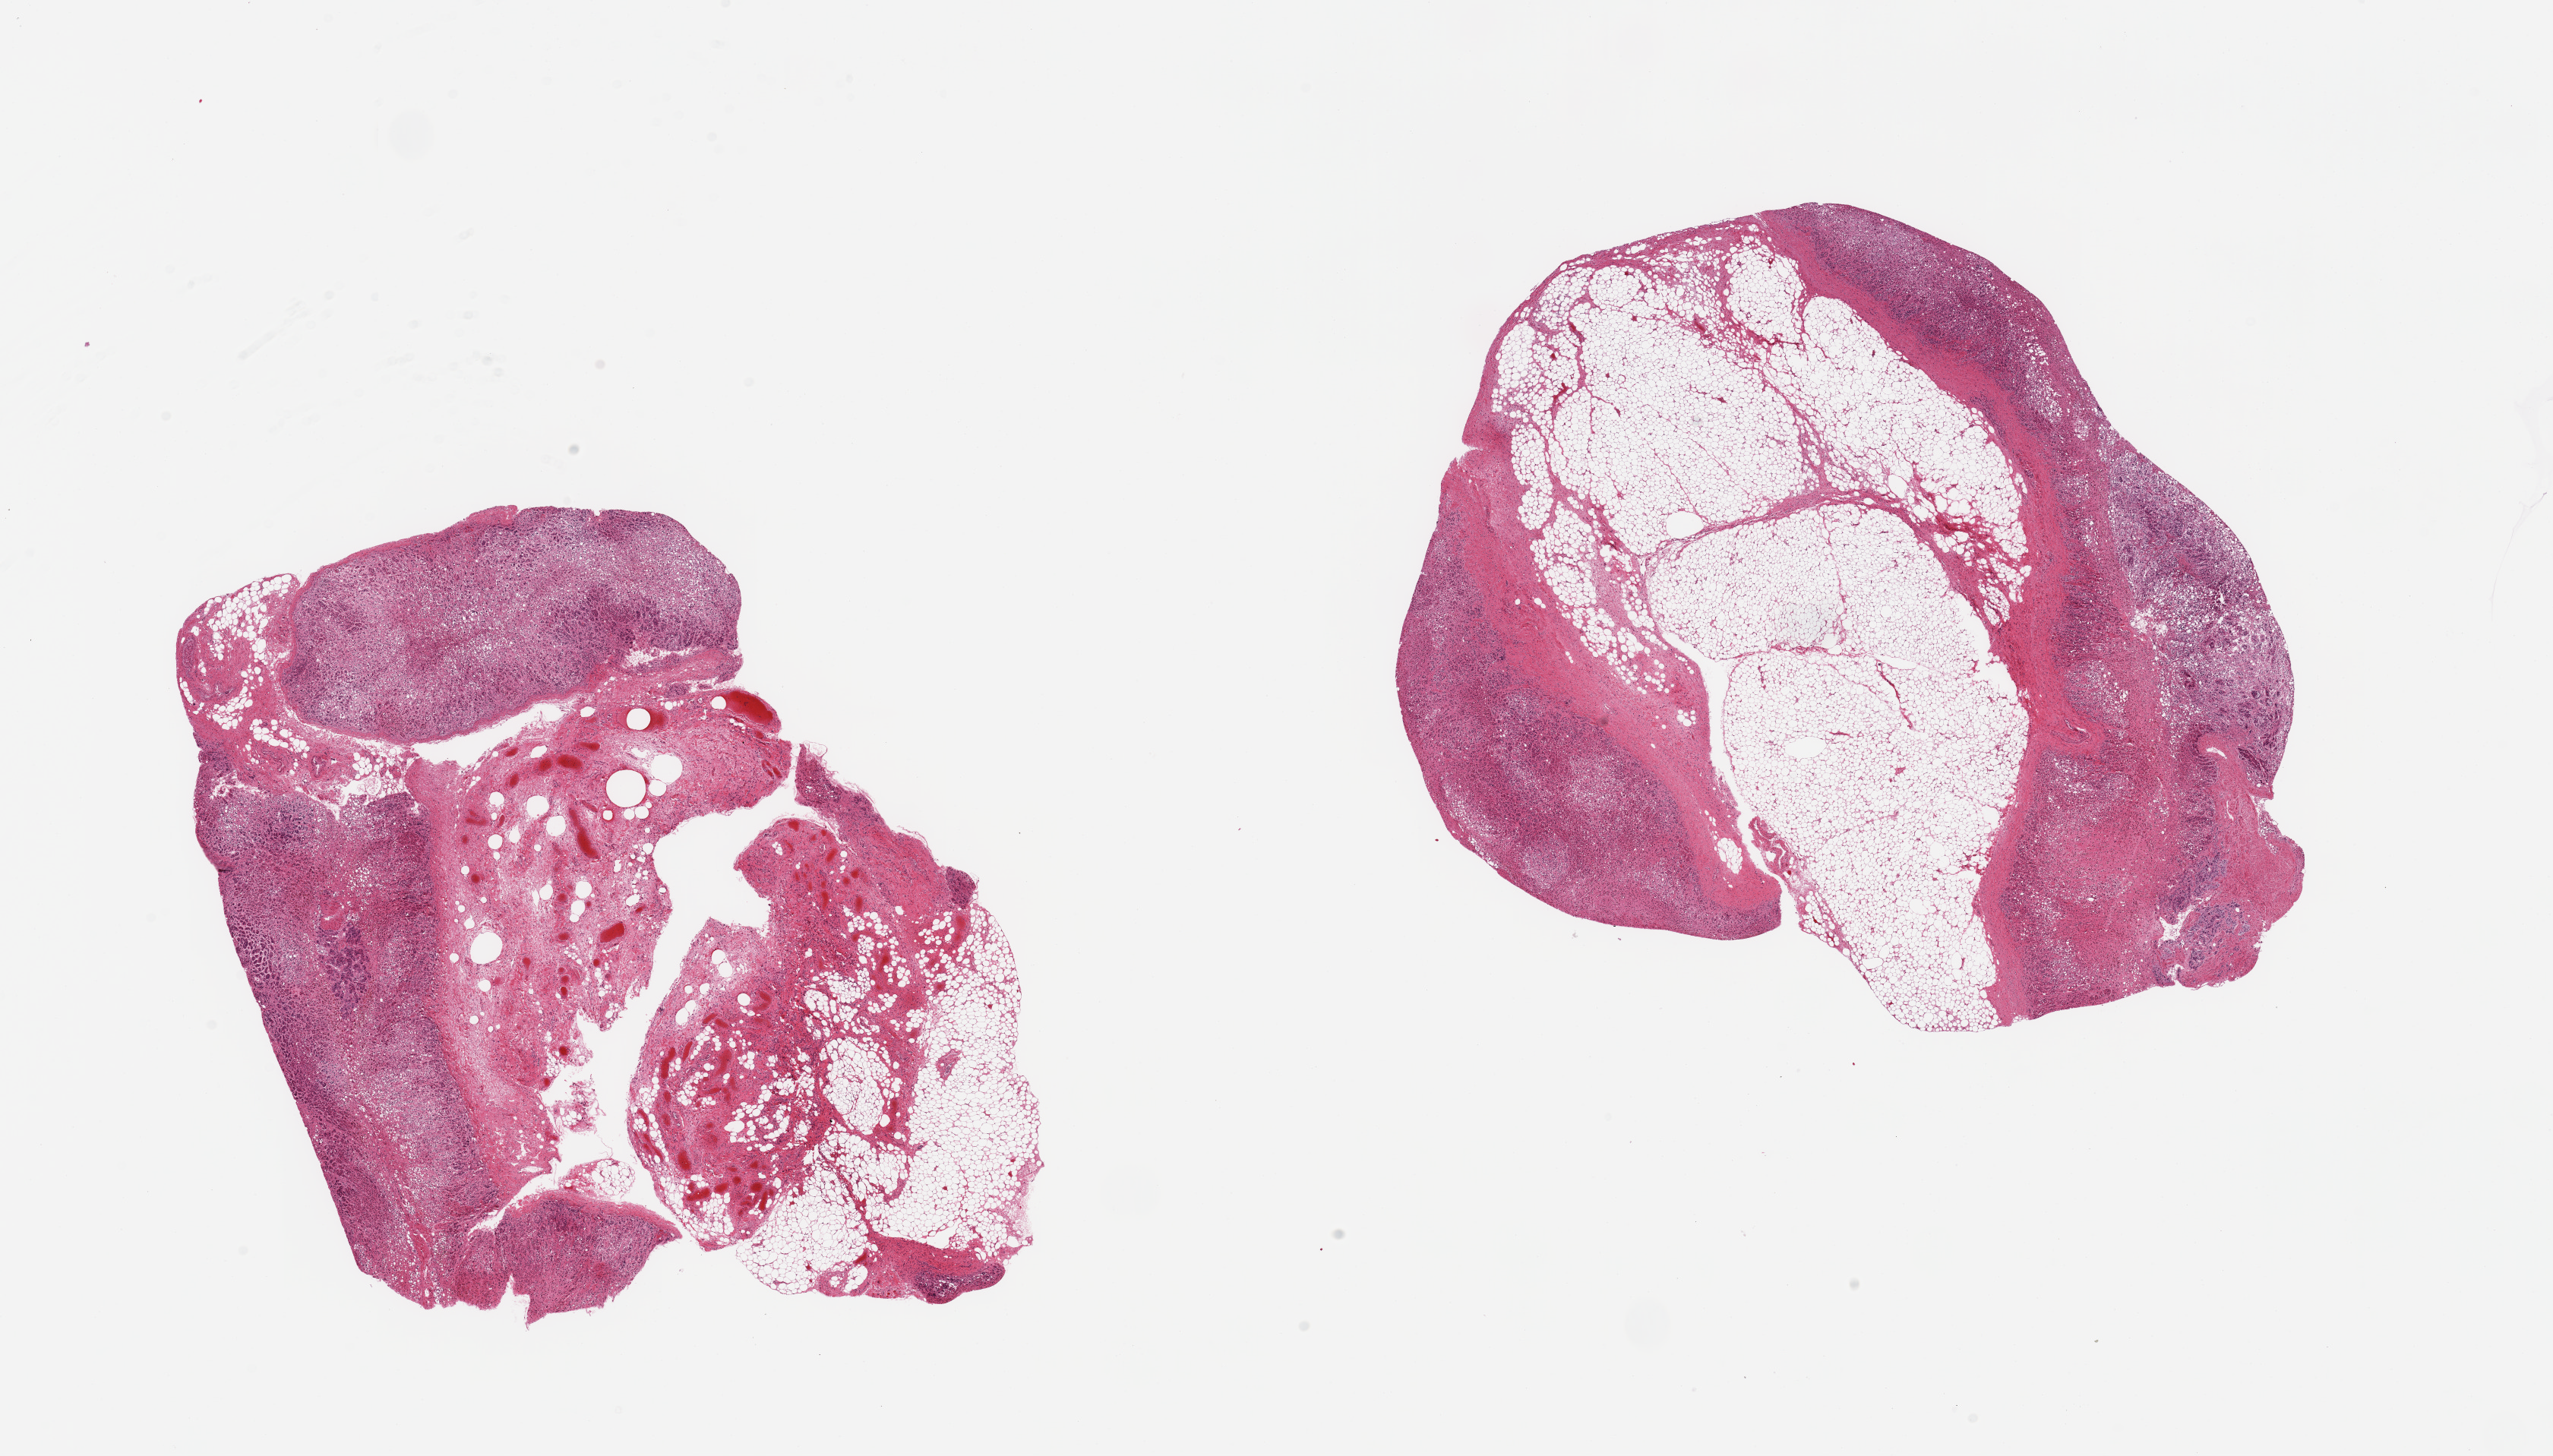
Digitized hematoxylin and eosin (H&E)-stained section — low-resolution overview of the scanned area, about 26.6 x 15.2 mm (acquisition: 20x scan); PAXgene-fixed paraffin-embedded (PFPE) section; target tissue: adrenal gland; donor tissue sample.
Review note (as recorded): 2 pieces; 60% fat content.